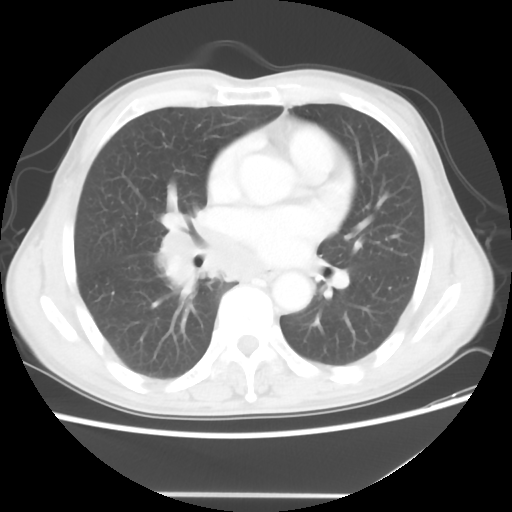
Chest CT, one axial slice. Position 27 of 56 along the scan axis. Lung window (W 1500 / L -600 HU). 512 × 512 image matrix, field of view 344 × 344 mm. Male patient, age 65 years. Case-level facts recorded for this patient, not image findings: clinical TNM (as recorded): T1c N3 M0; histopathological grade: G3.
Annotated regions visible in this slice (rectangle marked by the reading radiologist):
- lung tumour (recorded histology: small cell carcinoma): bounding box (x1, y1, x2, y2) in pixels: (154, 225, 281, 290)